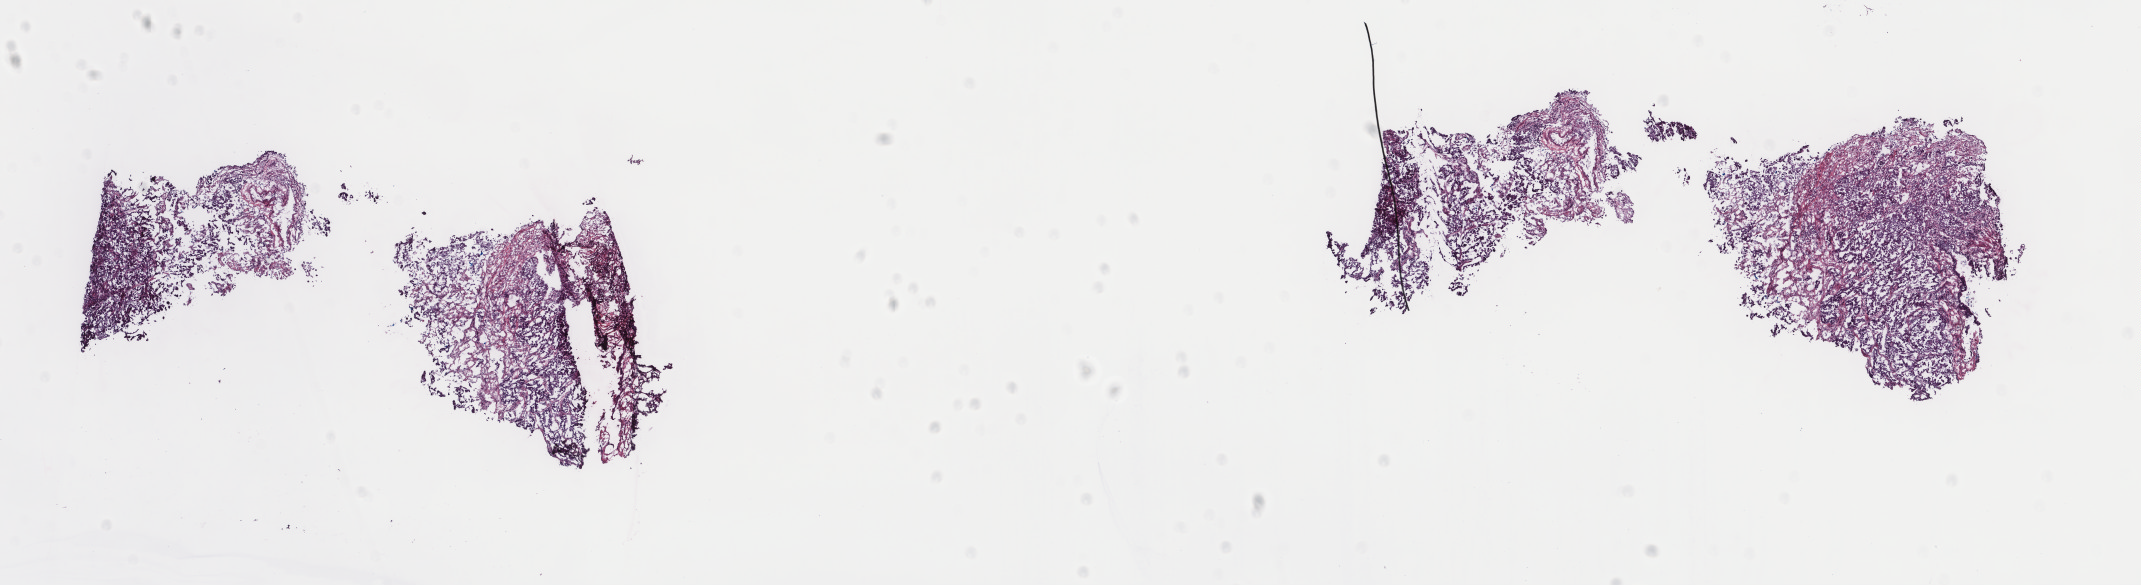
Whole-slide histology image, H&E — shown as a low-resolution overview of the whole scanned area (about 17.0 x 4.6 mm), frozen section, lung, primary tumour sample. Male, age 63 years at initial diagnosis. Slide review estimates, as recorded: tumour cells 100%, tumour nuclei 80%, normal cells 0%, stromal cells 0%, necrosis 0%. Inflammatory infiltration, as recorded: lymphocyte infiltration 2%, monocyte infiltration 2%, neutrophil infiltration 0%.
AJCC pathologic stage: IA (7th edition). Pathologic diagnosis: Adenocarcinoma, NOS (upper lobe, lung). Laterality: left.